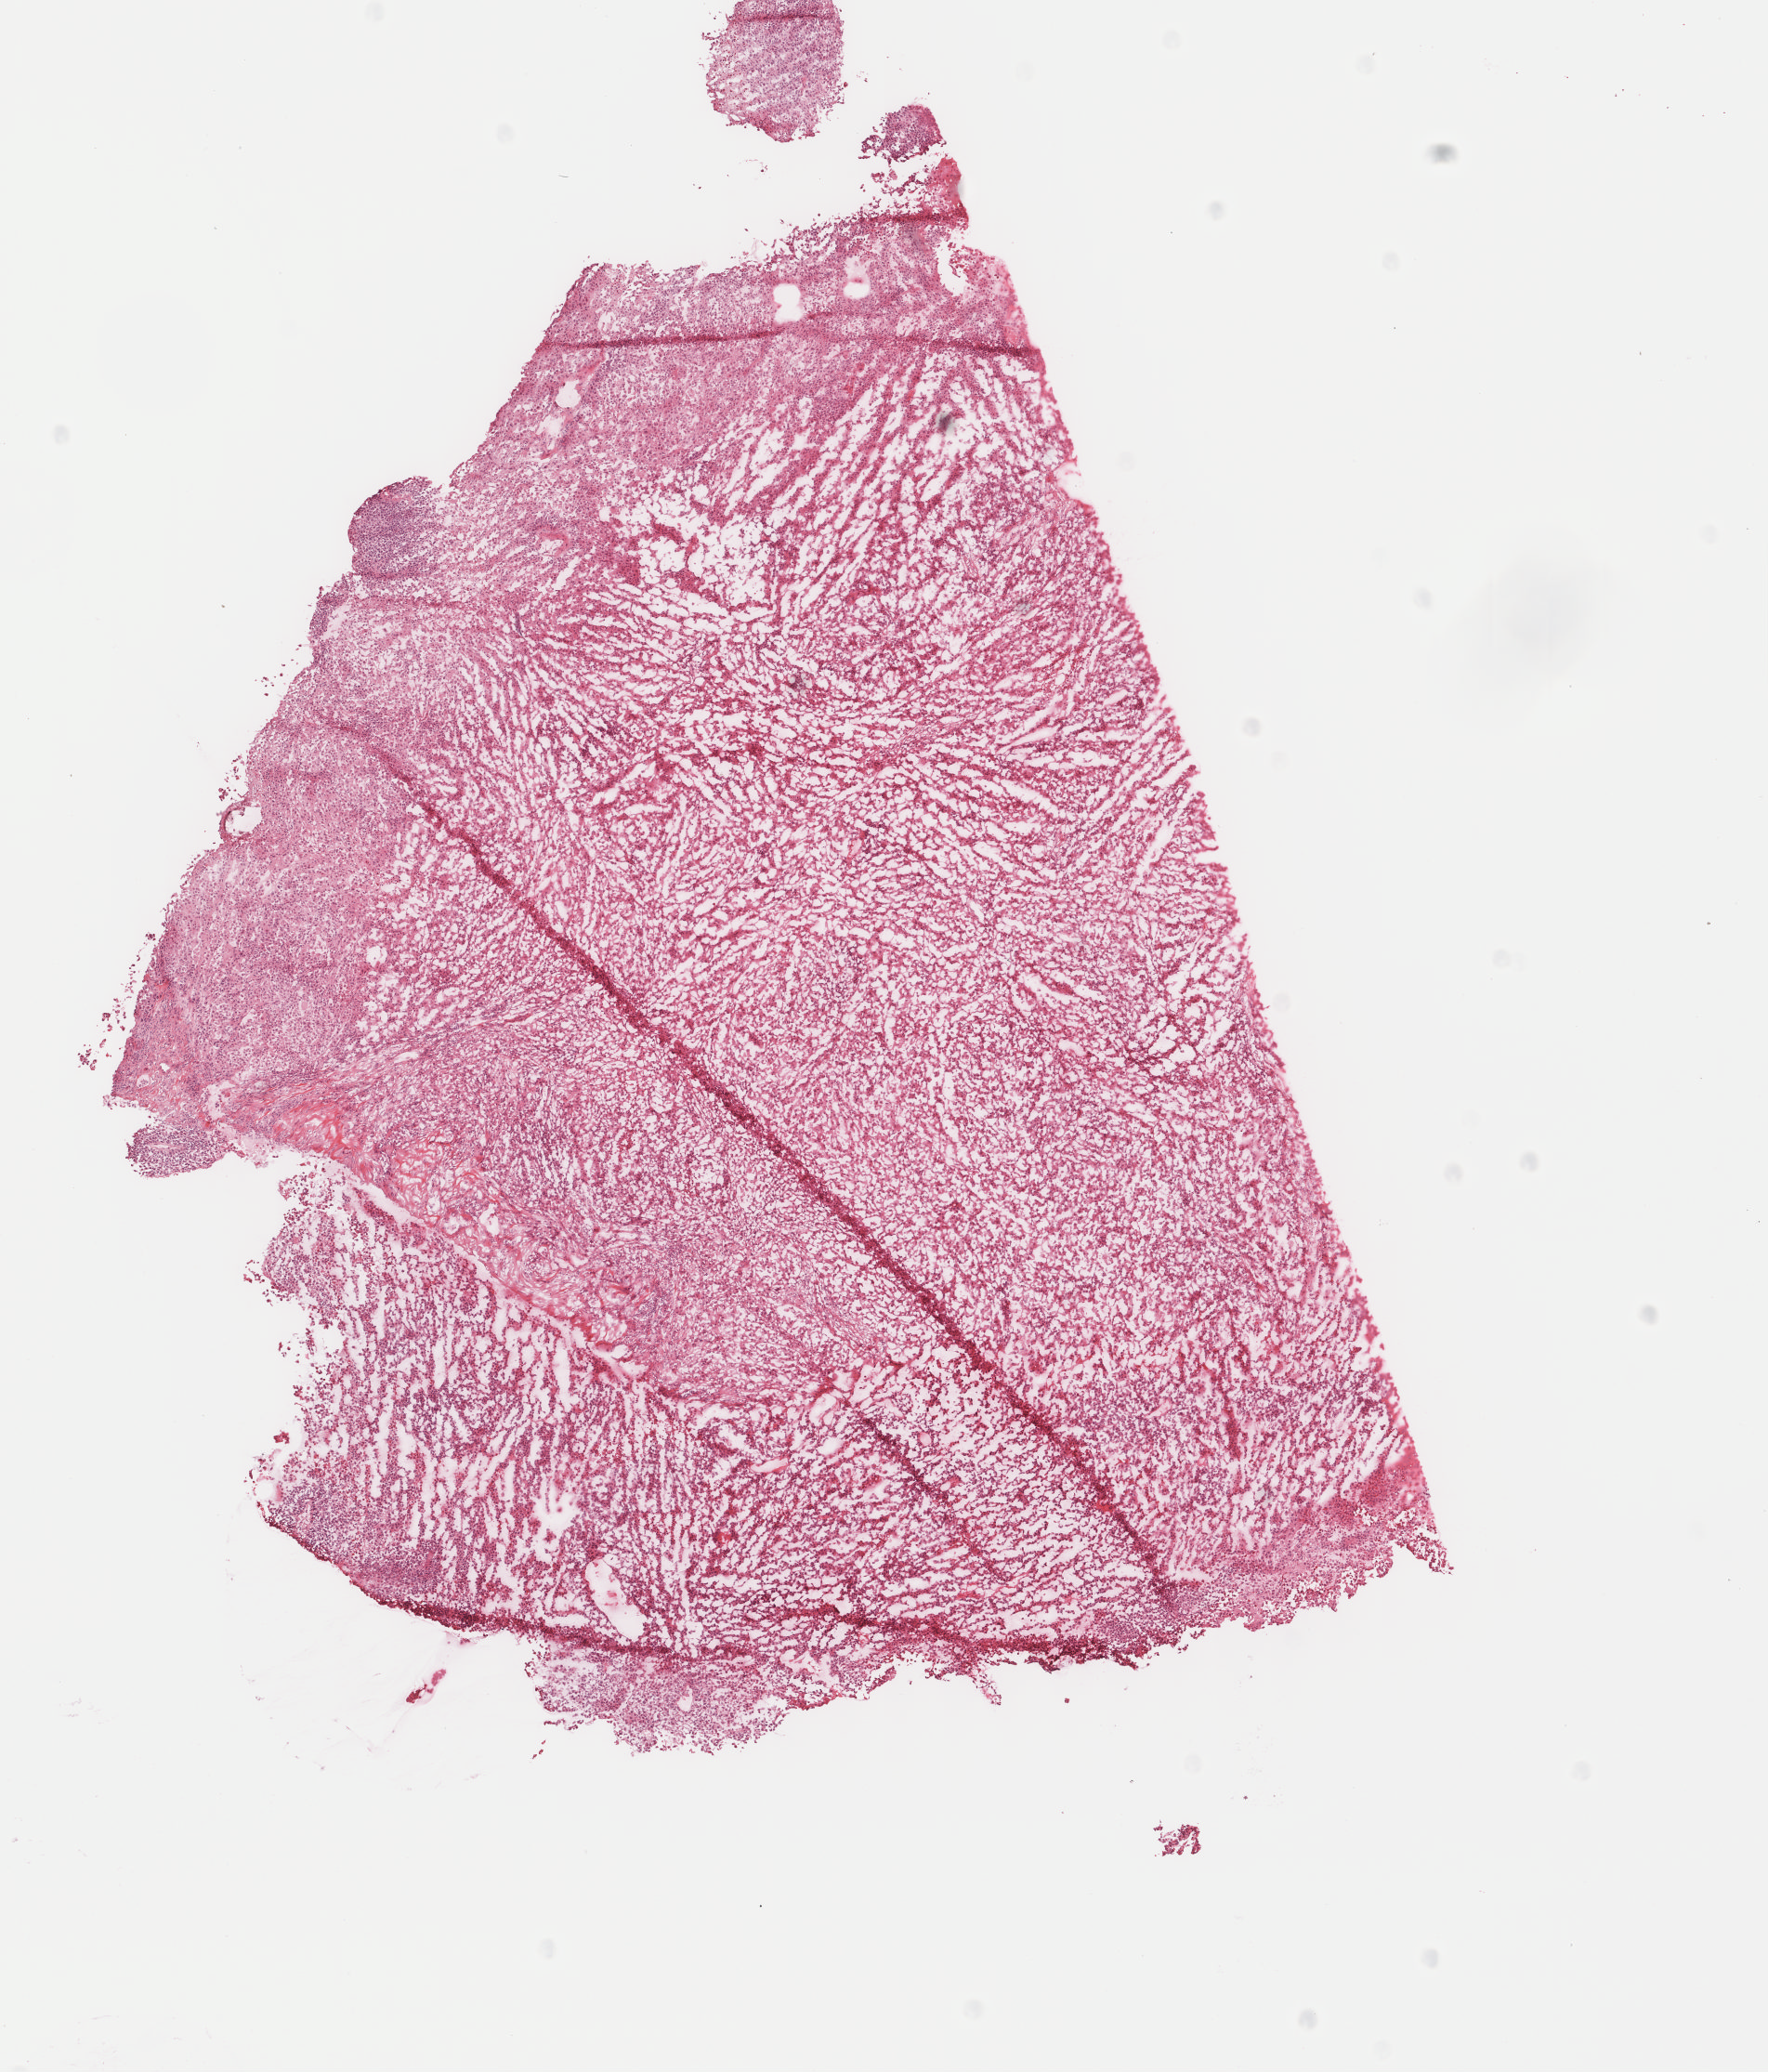
H&E-stained whole-slide image — whole scanned area (about 7.6 x 8.9 mm, acquisition: 40x scan) shown as a low-resolution overview. Formalin-fixed paraffin-embedded (FFPE) diagnostic section. Sample: primary tumour, skin. Female patient; age at initial diagnosis 40 years.
• pathologic diagnosis: Malignant melanoma, NOS